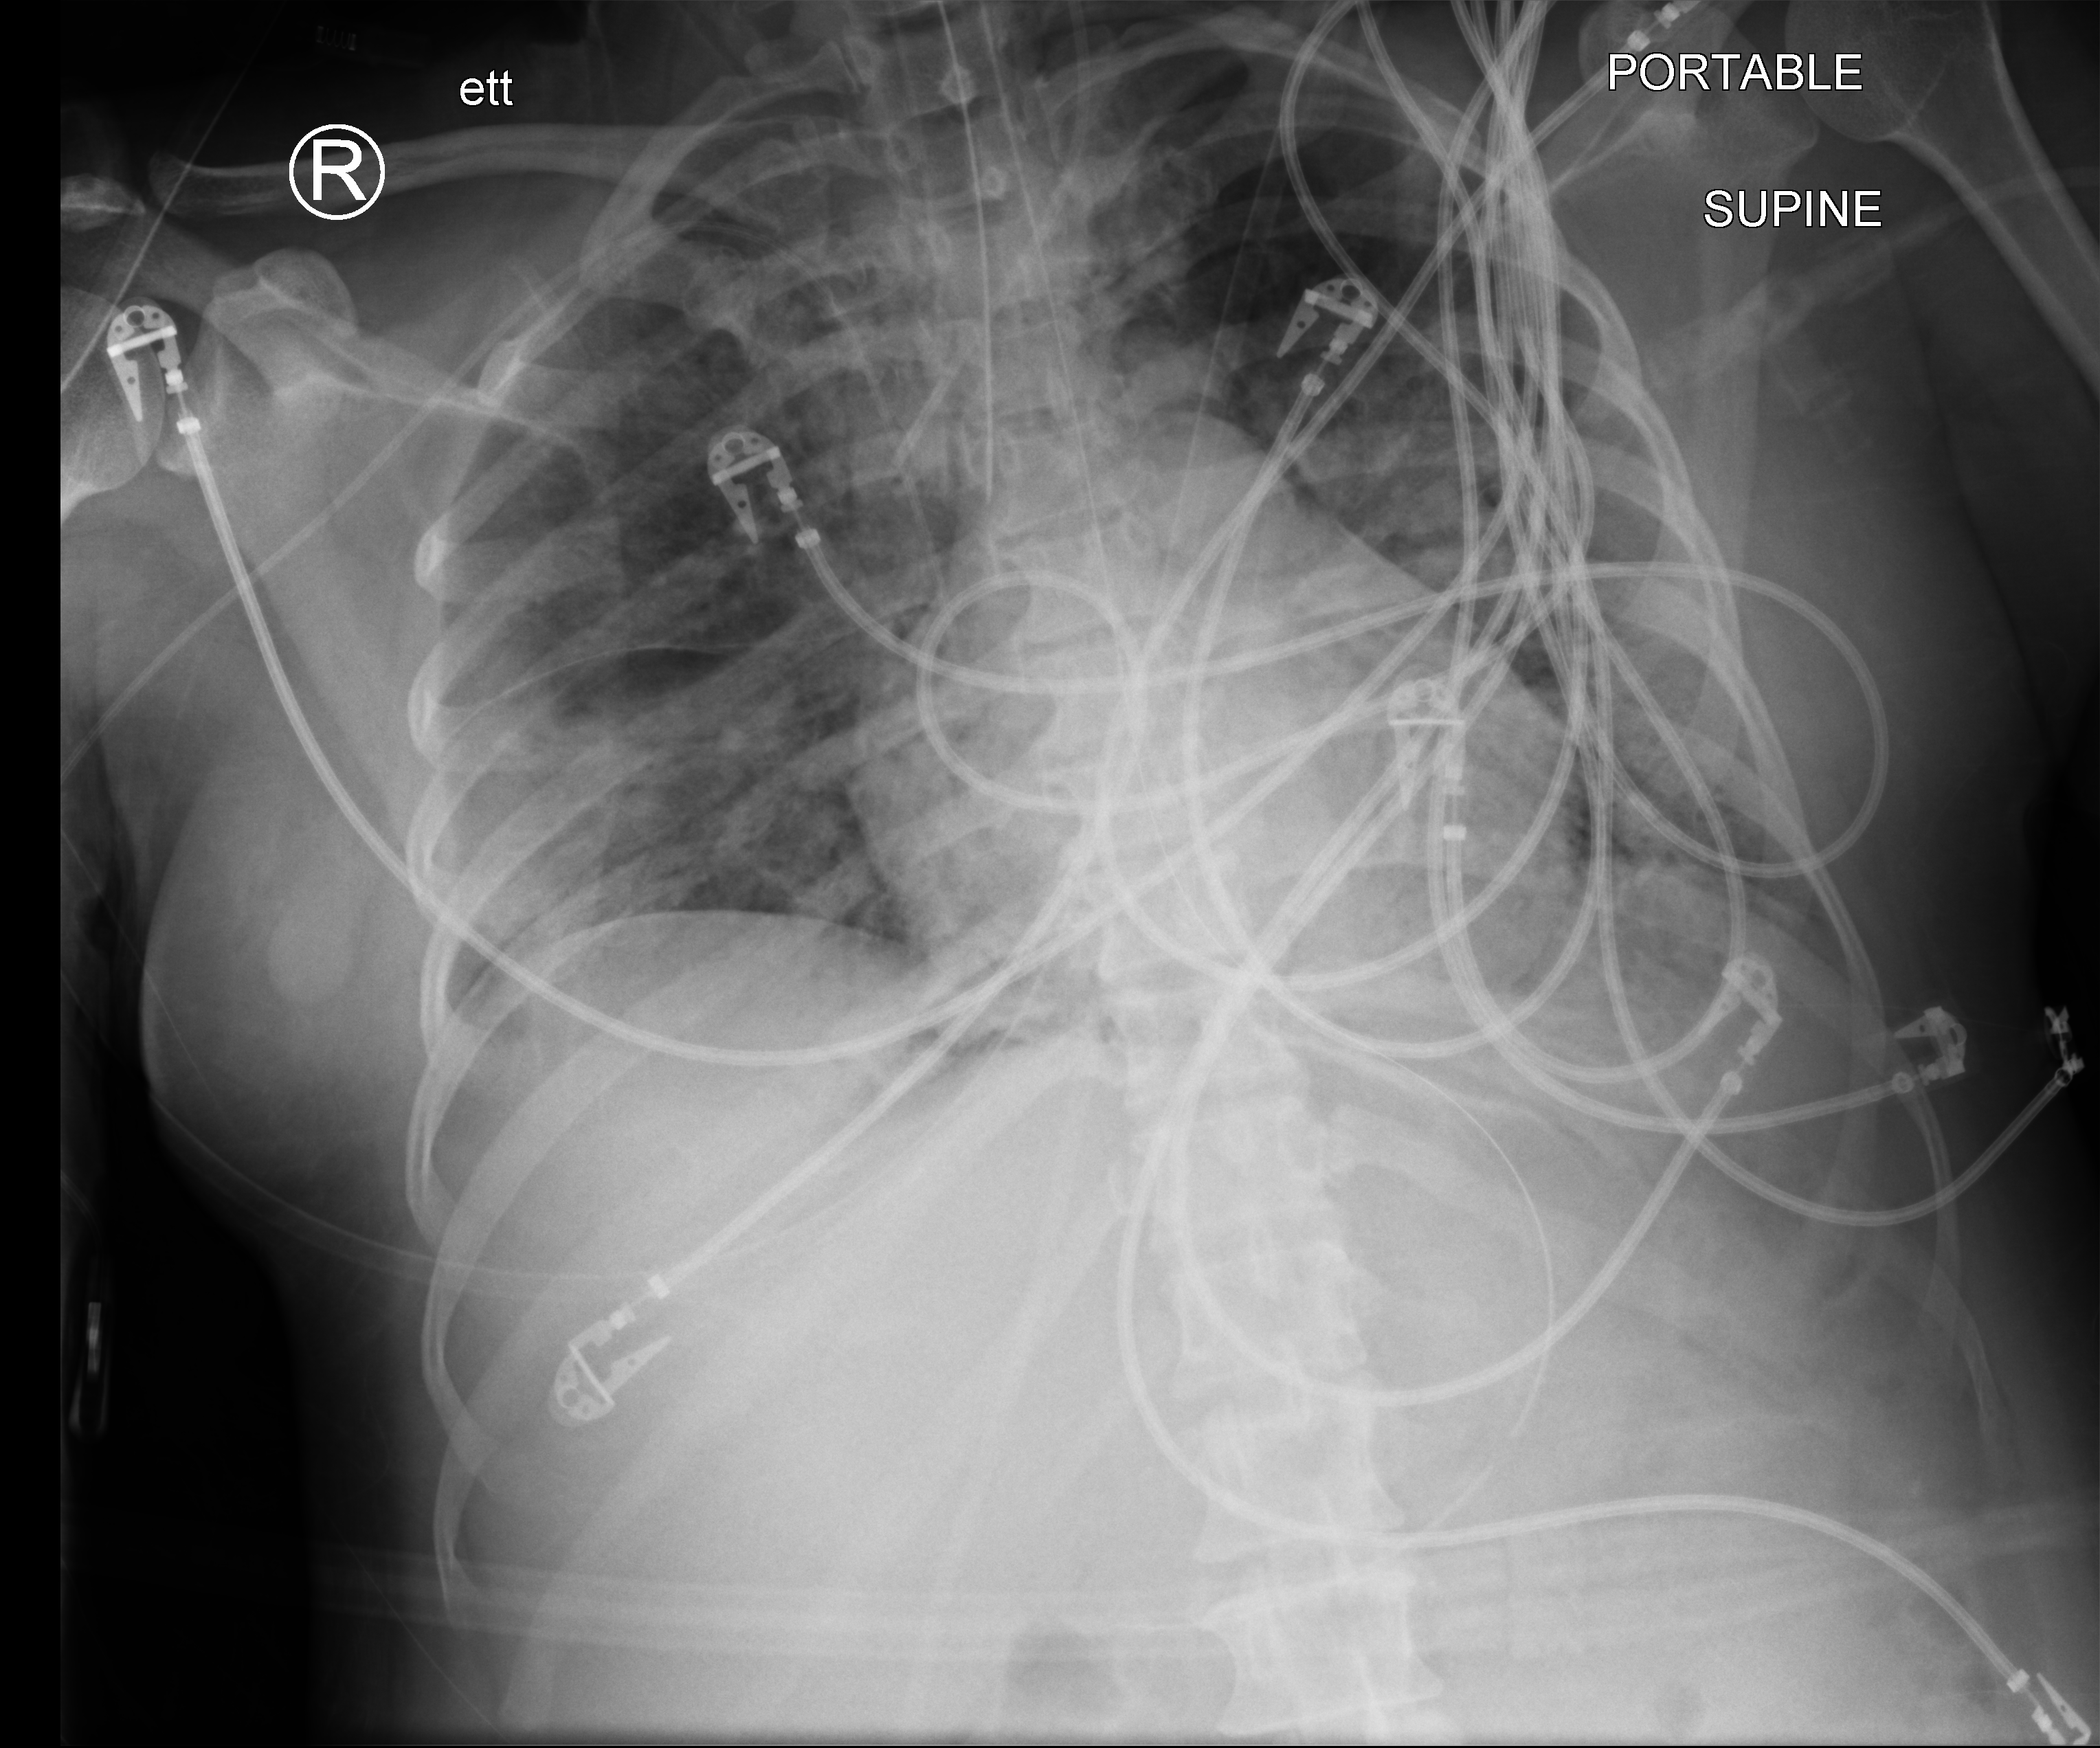
Chest X-ray (portable); anteroposterior (AP) projection. Patient hospitalised with COVID-19; female, aged 18–59 years.
Admission-level facts for this patient (not findings on this image; timing relative to this image not recorded):
- mechanically ventilated during this hospital stay: yes
- admitted to intensive care during this hospital stay: yes